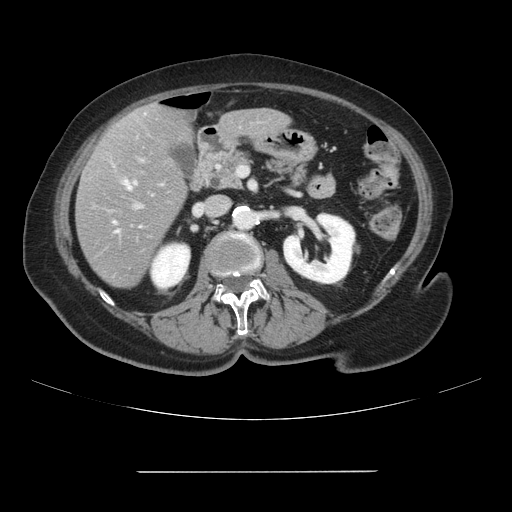
Contrast-enhanced abdominal CT, one axial slice; slice 37 of 111 in the series (ordered by position); 120 kVp; intravenous contrast given; soft-tissue window (W 400 / L 40 HU); 2.5 mm slice thickness; 512 × 512 image matrix. Female patient, age 74 years. From the clinical record (not read from this slice): diagnosis: colorectal cancer liver metastases, imaged before liver resection; multiple liver metastases: yes; largest metastasis: 1.1 cm; disease in both lobes: yes.
Outlined on this slice (outlined manually by an expert reader):
- hepatic veins: bounding box (x1, y1, x2, y2) in pixels: (125, 181, 131, 189)
- liver: (76, 104, 290, 287)
- planned liver remnant (the part of the liver to remain after resection): (140, 104, 289, 144)